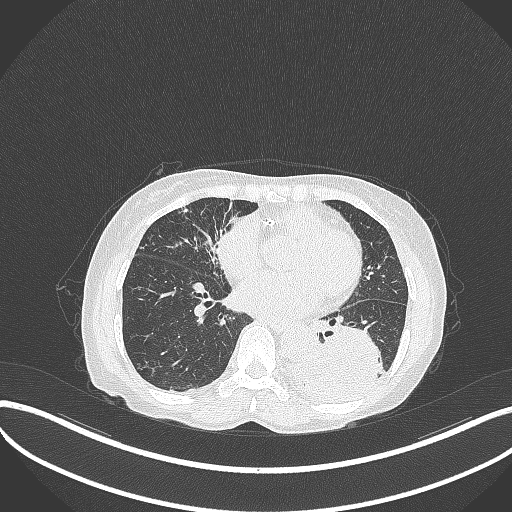
Chest CT, one axial slice; slice 126 of 370 in the series (ordered by position); lung window (W 1500 / L -600 HU); 1 mm slice thickness; 512 × 512 image matrix. Patient: female, 78 years. Case-level facts recorded for this patient, not image findings: clinical TNM (as recorded): T3 N0 M1.
Annotated regions visible in this slice (bounding box drawn by a radiologist):
- lung tumour (recorded histology: squamous cell carcinoma): bounding box <292,325,387,405> (left, top, right, bottom; pixels)